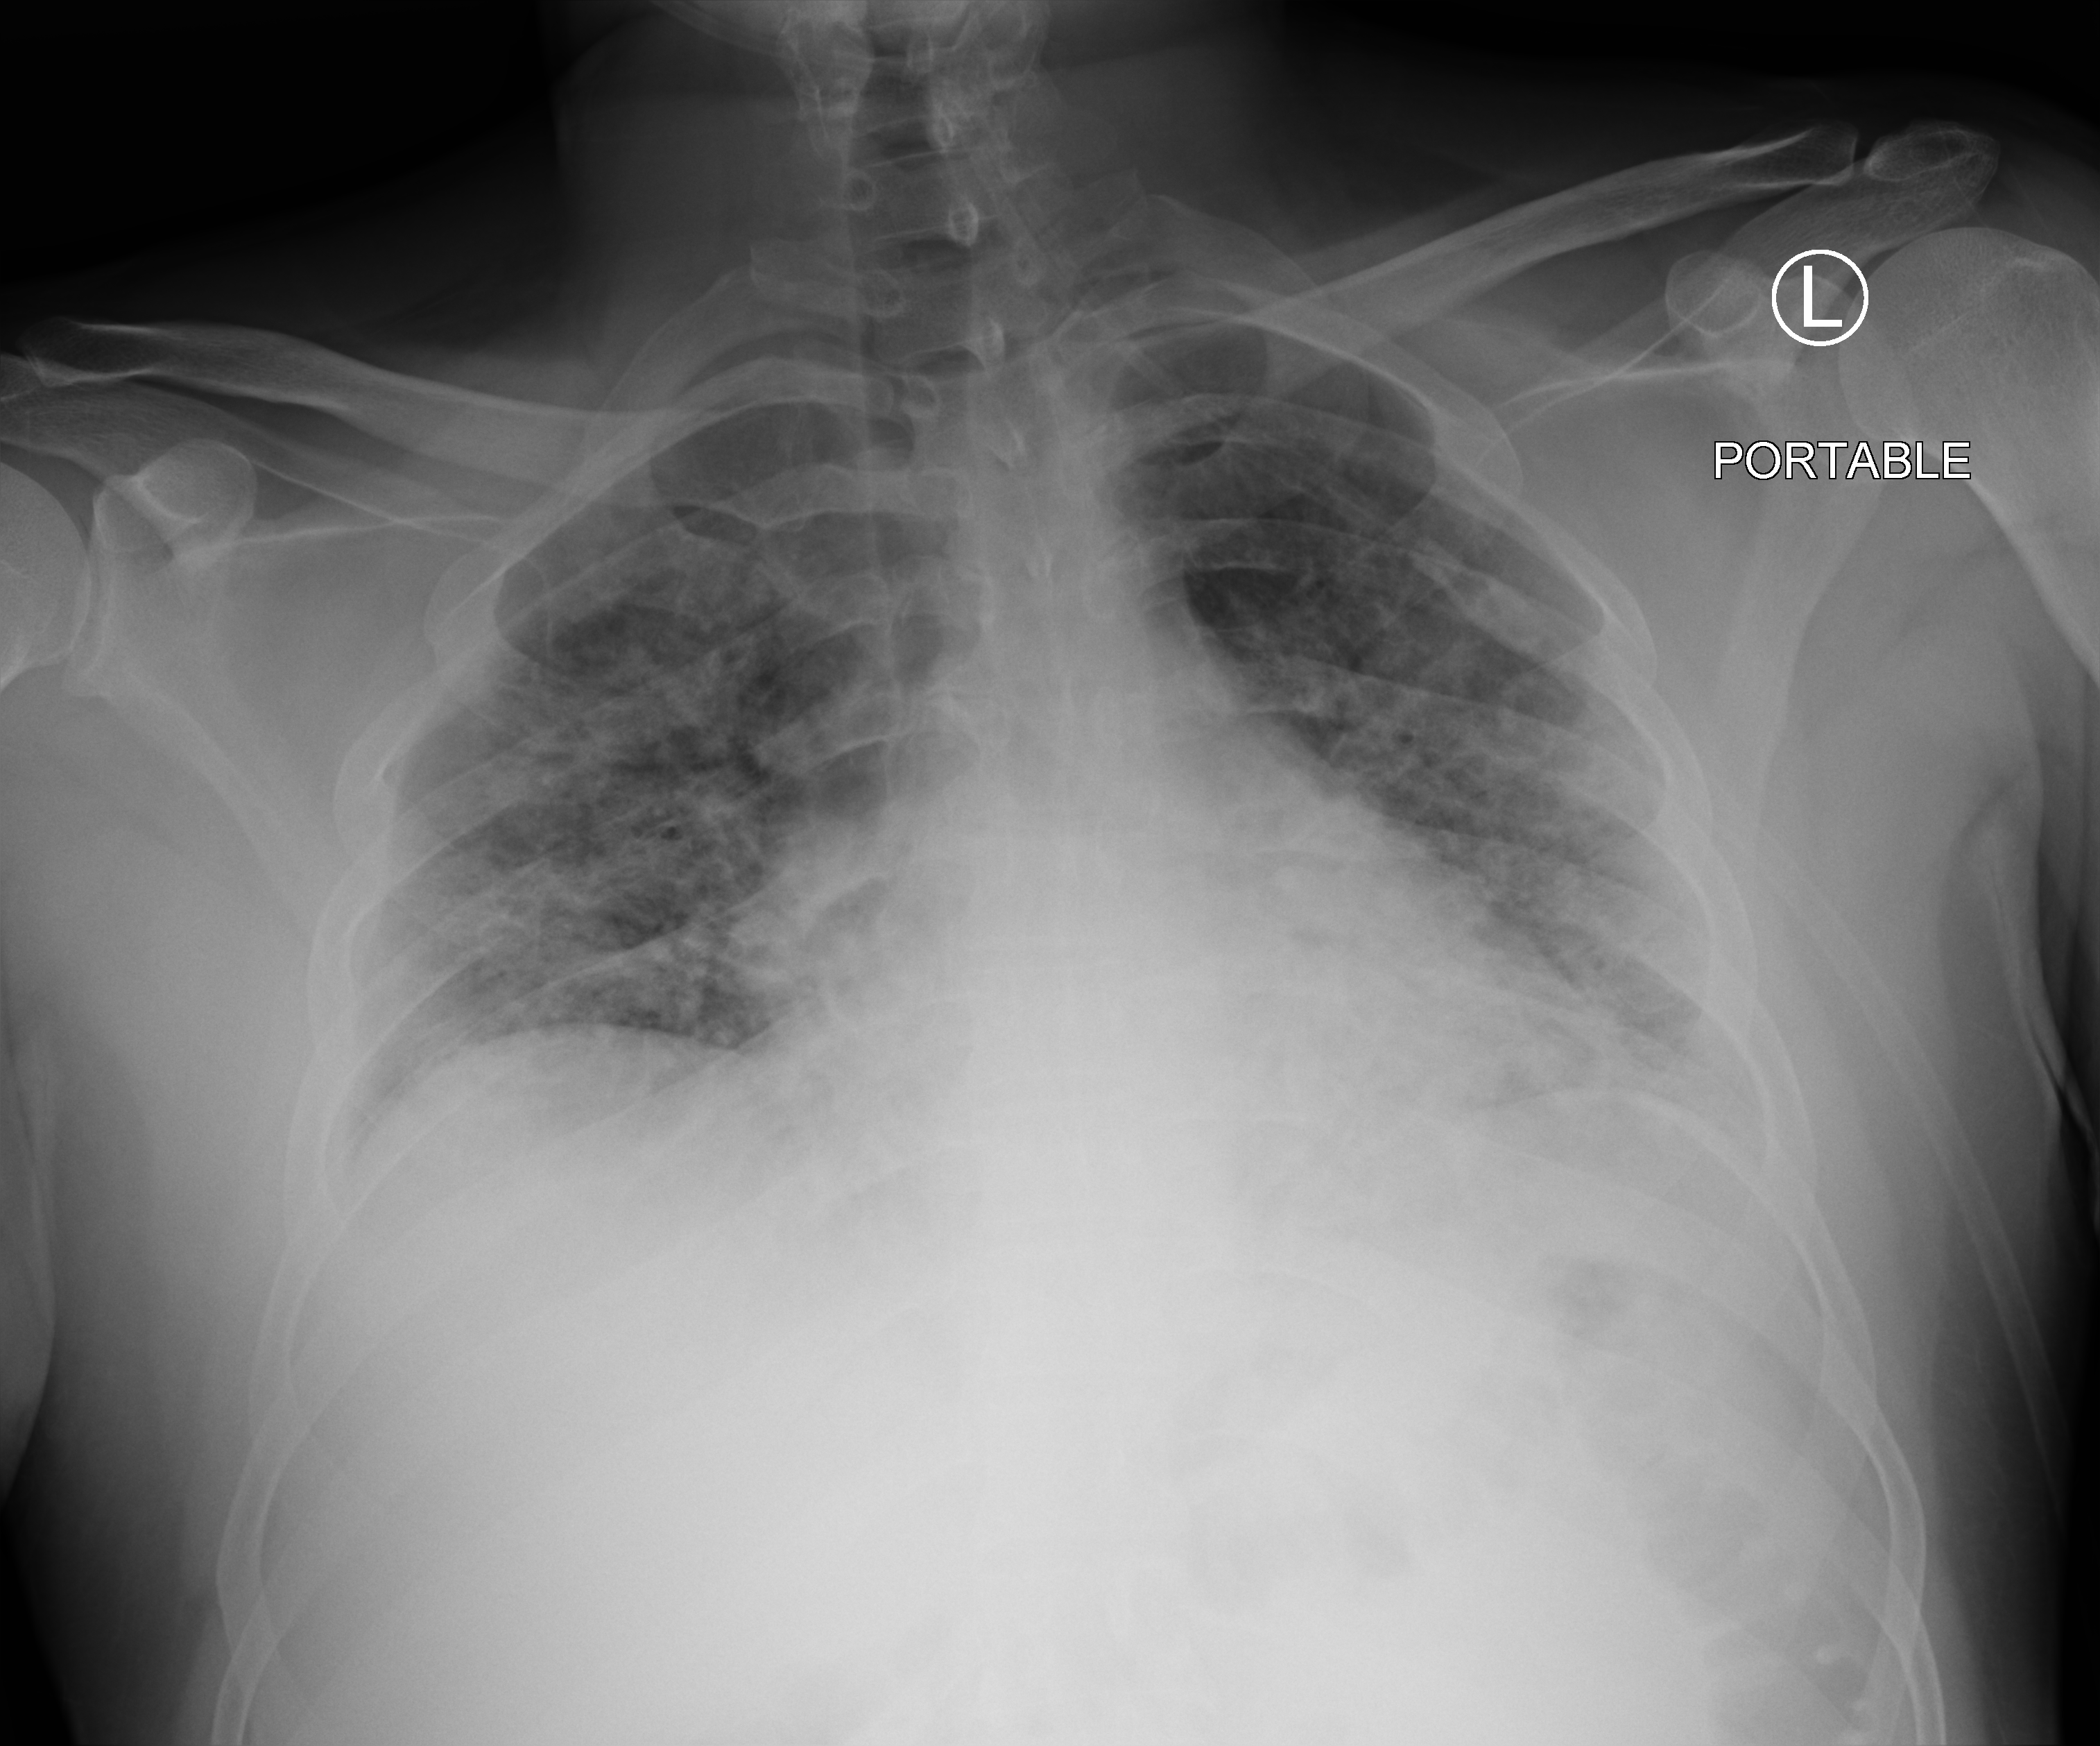
Chest X-ray (portable). Male patient hospitalised with COVID-19, age 18–59 years.
Hospital-stay facts (about this admission, not read from this image; timing relative to this image not recorded):
- length of hospital stay: 6 days
- admitted to intensive care during this hospital stay: no